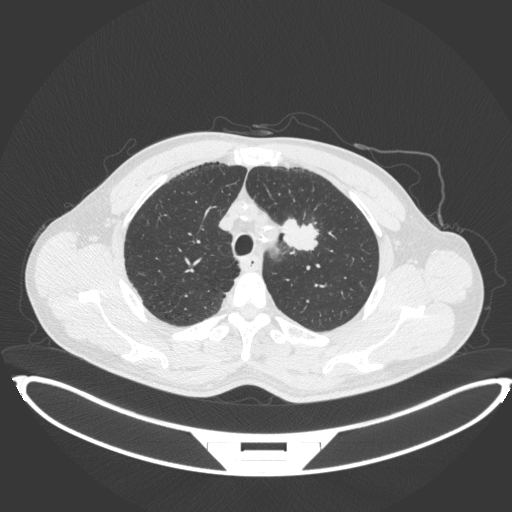
Chest CT, one axial slice. Position 342 of 407 along the scan axis. 120 kVp. Lung window (W 1500 / L -600 HU). 1 mm slice thickness. 512 × 512 image matrix, field of view 457 × 457 mm. Male patient, age 60 years. Case-level facts recorded for this patient, not image findings: clinical TNM (as recorded): T2a N0 M0; histopathological grade: G1-G2.
Structures marked on this image (rectangle marked by the reading radiologist):
- lung tumour (recorded histology: squamous cell carcinoma): bounding box <278,213,322,254> (left, top, right, bottom; pixels)